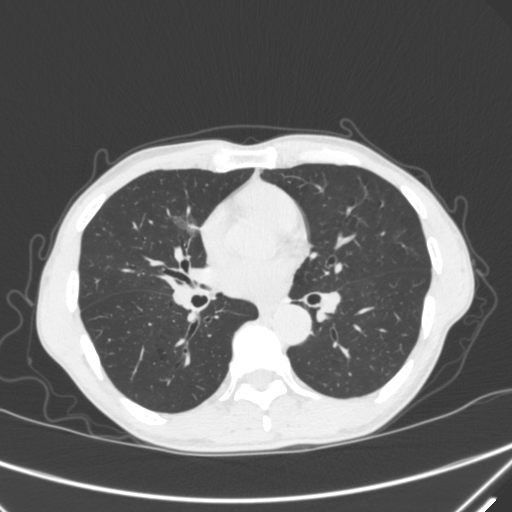
Chest CT, one axial slice. Slice 171 of 340 in the series (ordered by position). Lung window (W 1500 / L -600 HU). 1 mm slice thickness. 512 × 512 image matrix, field of view 350 × 350 mm. Male patient, age 67 years. Case-level facts recorded for this patient, not image findings: clinical TNM (as recorded): T1c N0 M0; histopathological grade: G1-2.
Structures marked on this image (rectangle marked by the reading radiologist):
- lung tumour (recorded histology: adenocarcinoma): bounding box <162,204,211,256> (left, top, right, bottom; pixels)